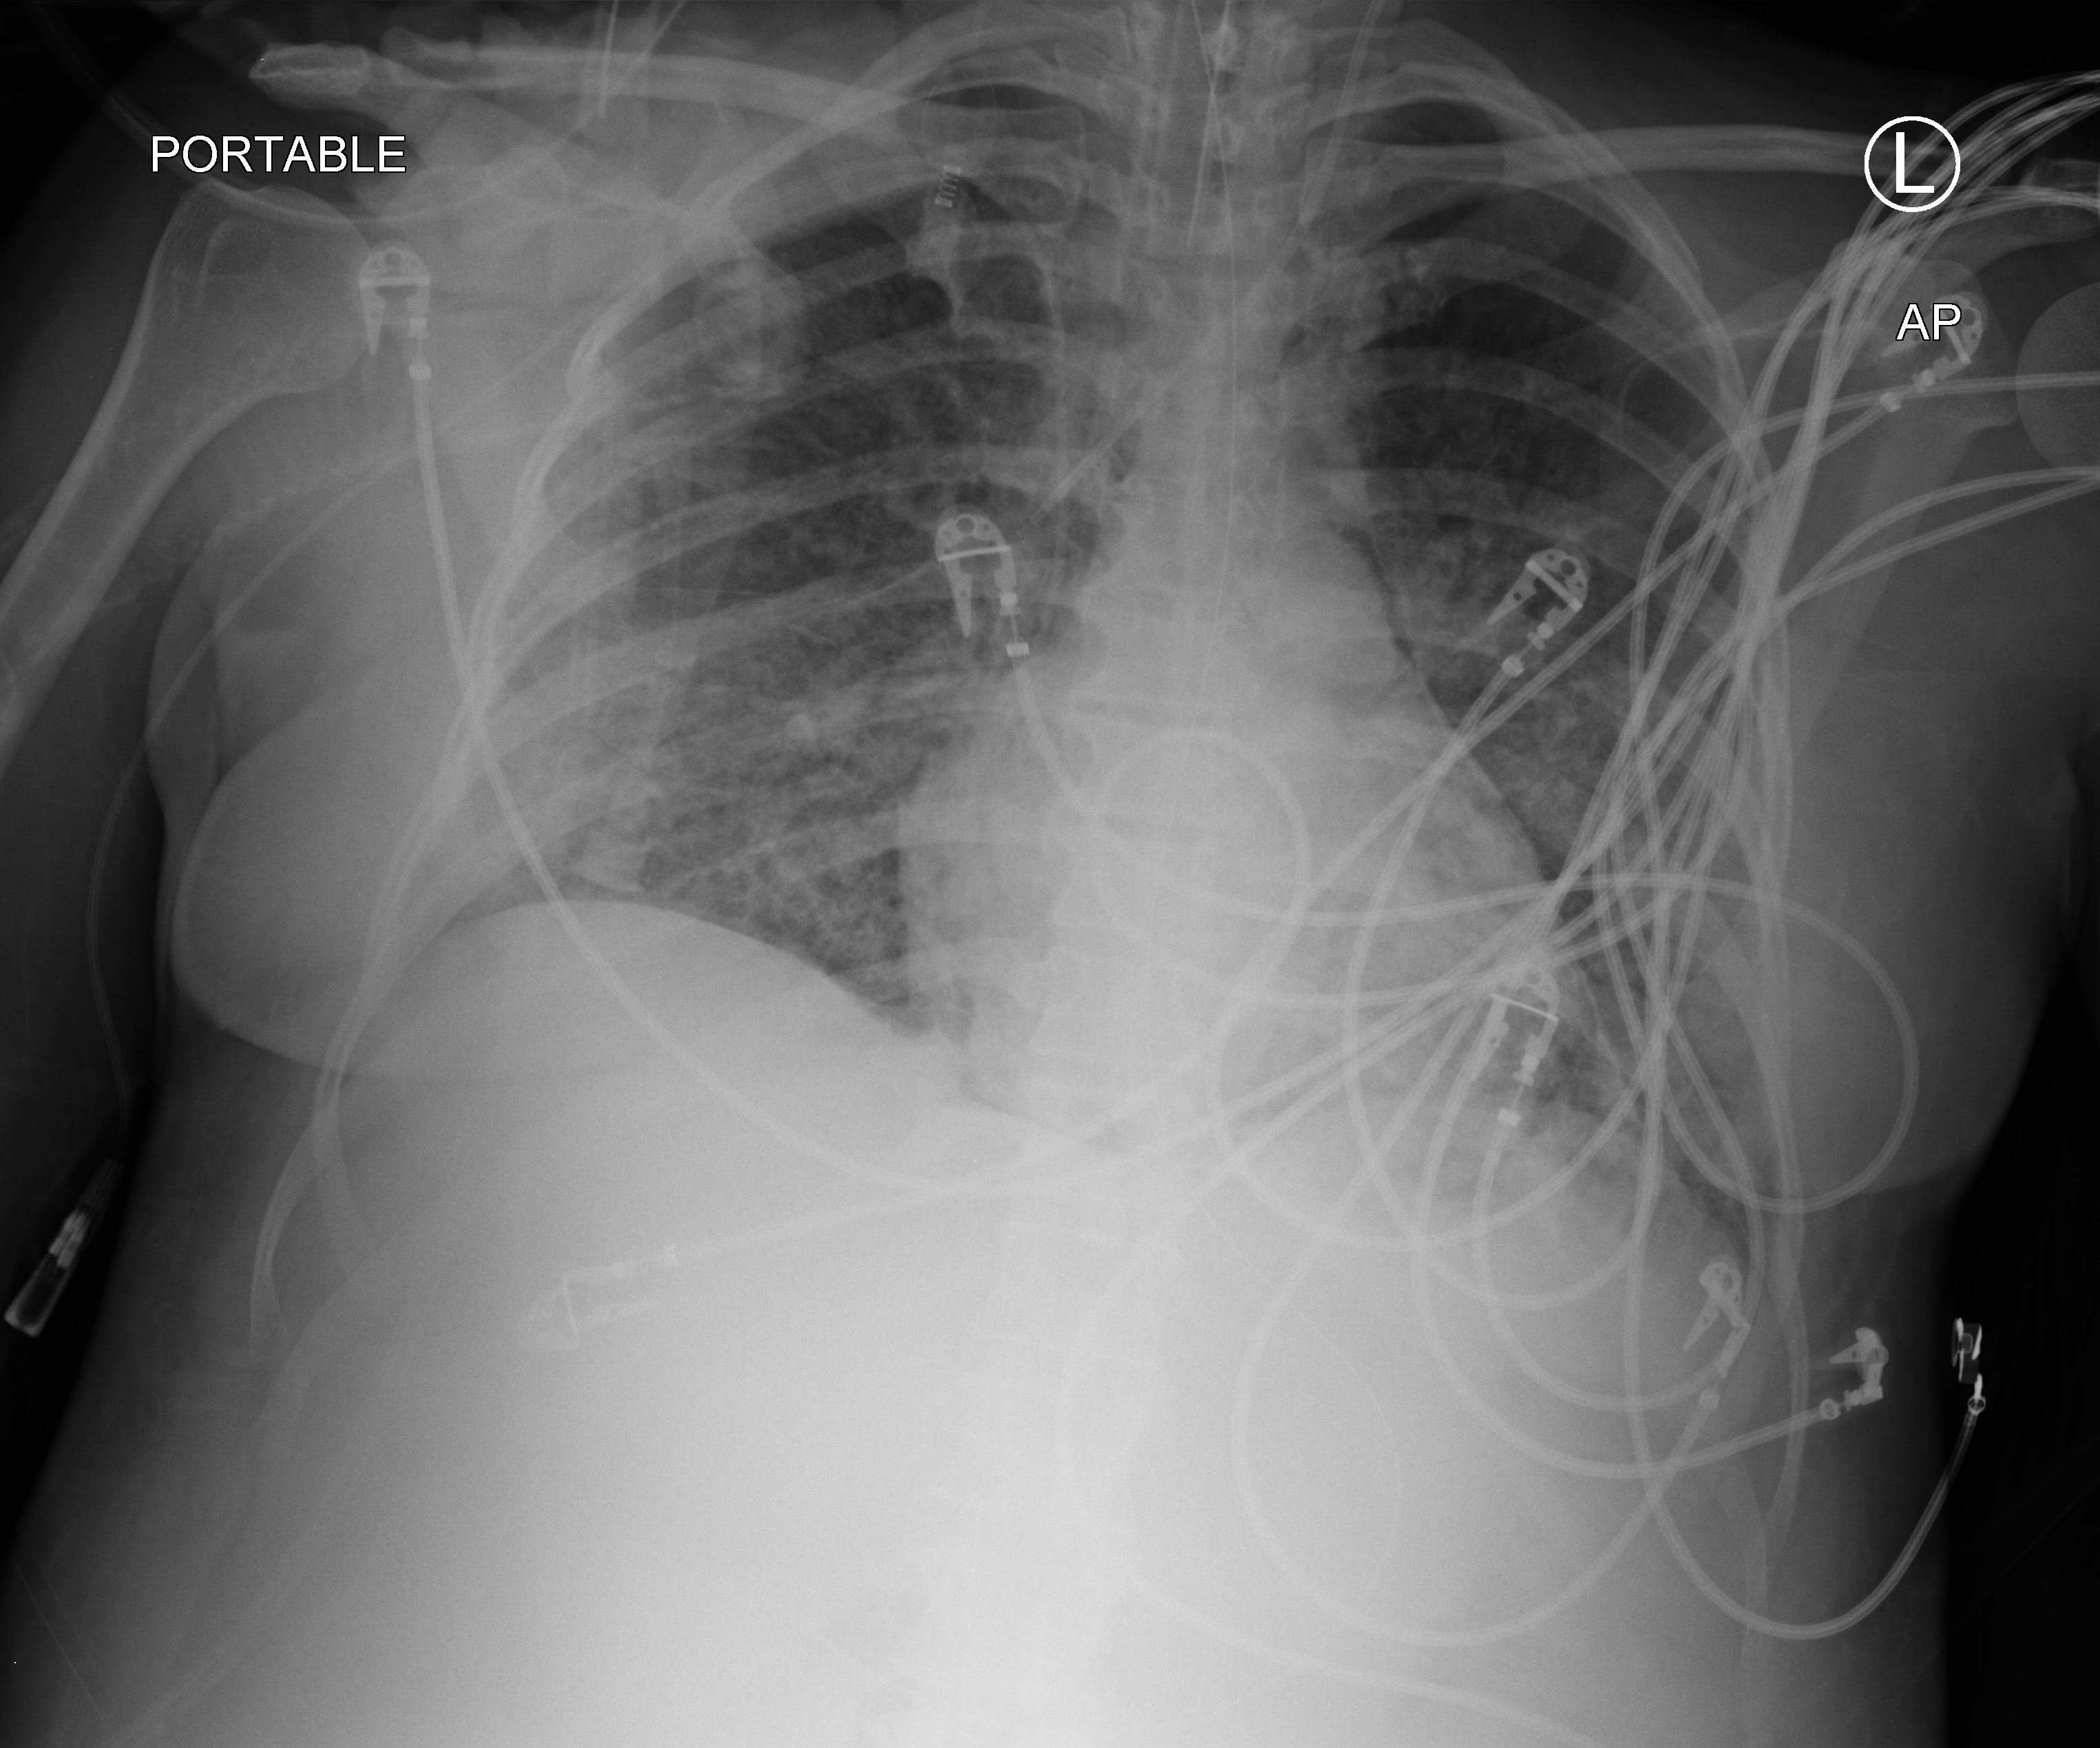
Bedside chest radiograph (computed radiography); anteroposterior (AP) projection. Patient hospitalised with COVID-19; female, aged 18–59 years.
Hospital-stay facts (about this admission, not read from this image; timing relative to this image not recorded):
- length of hospital stay: 71 days
- mechanically ventilated during this hospital stay: yes